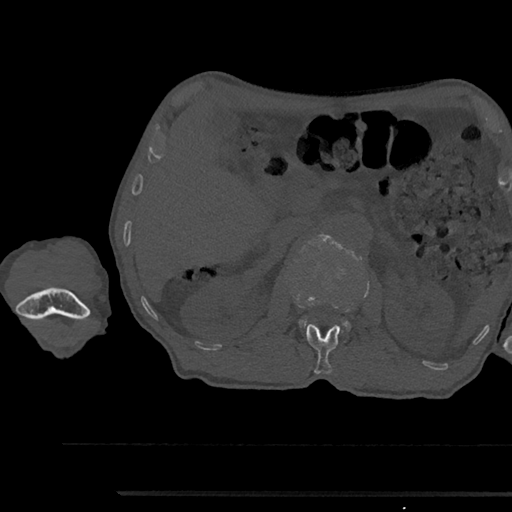
CT including the spine, one axial slice; slice 611 of 797 in the series (ordered by position); 120 kVp; bone window (W 1800 / L 400 HU); 0.5 mm slice thickness; 512 × 512 image matrix, field of view 367 × 367 mm. Male patient, age 79 years. Case-level facts recorded for this patient, not image findings: primary cancer: prostate.
Outlined on this slice (semi-automatically segmented with operator editing):
- L1 vertebra: bounding box <306,324,340,374> (left, top, right, bottom; pixels)
- L2 vertebra: <299,234,350,329>